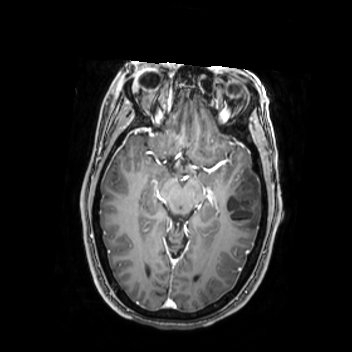
Brain MRI from a brain-tumour surgery series, one axial slice; slice 154 of 350 in the series (ordered by position); T1-weighted post-contrast; 352 × 352 image matrix, field of view 280 × 280 mm. Case-level facts recorded for this patient, not image findings: histopathology: Oligodendroglioma; WHO grade: 2; IDH mutation: yes.
Structures marked on this image (manually delineated by an expert):
- tumour: bounding box (x1, y1, x2, y2) in pixels: (224, 171, 262, 232)